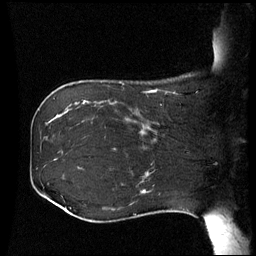
Breast MRI (dynamic contrast-enhanced), one sagittal slice; slice 17 of 60 in the series (ordered by position); dynamic contrast-enhanced series, image 2 of 3 at this slice position (ordered by acquisition); 1.5 T; TE 4.2 ms, TR 8.9 ms; 2.5 mm slice thickness; 256 × 256 image matrix, field of view 230 × 230 mm. Patient: female, 42 years. From the clinical record (not read from this slice): setting: breast cancer imaged before/during neoadjuvant chemotherapy; receptor status: HER2-positive.
Annotated regions visible in this slice (semi-automatic segmentation, software-assisted and operator-edited):
- analysis volume of interest (the breast-tissue region the enhancement analysis was run in; not a lesion): box from (x=106, y=102) to (x=173, y=150) px
- tumour enhancement mask (voxels above the 70 % enhancement threshold inside the analysis volume of interest): (x=154, y=104)–(x=162, y=132)